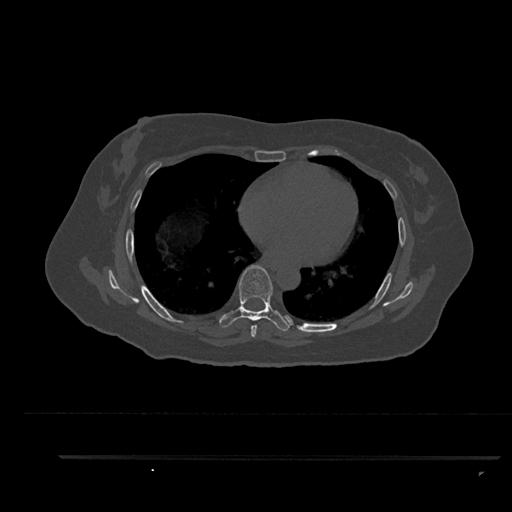
CT including the spine, one axial slice; position 516 of 797 along the scan axis; bone window (W 1800 / L 400 HU); 0.5 mm slice thickness; 512 × 512 image matrix, field of view 408 × 408 mm. Patient: female, 44 years. Case-level facts recorded for this patient, not image findings: primary cancer: renal.
Structures marked on this image (semi-automatically segmented with operator editing):
- T6 vertebra: bounding box <251,320,257,337> (left, top, right, bottom; pixels)
- T7 vertebra: <219,265,292,331>